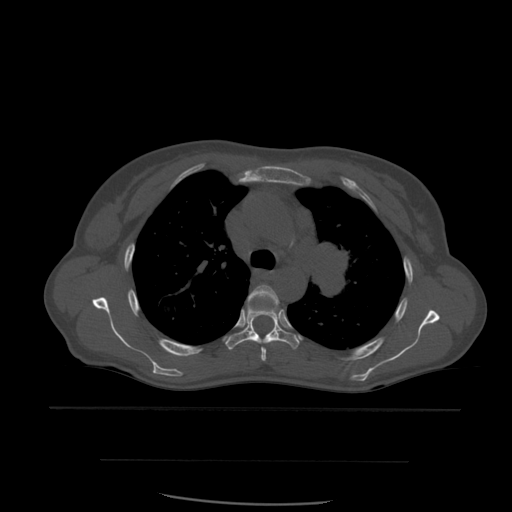
CT including the spine, one axial slice. Slice 415 of 574 in the series (ordered by position). Bone window (W 1800 / L 400 HU). 1.25 mm slice thickness. 512 × 512 image matrix, field of view 392 × 392 mm. Patient age 48 years. From the clinical record (not read from this slice): primary cancer: lung.
Annotated regions visible in this slice (semi-automatic segmentation, software-assisted and operator-edited):
- T4 vertebra: bounding box [x1, y1, x2, y2] px = [248, 285, 280, 362]
- T5 vertebra: [226, 301, 300, 350]